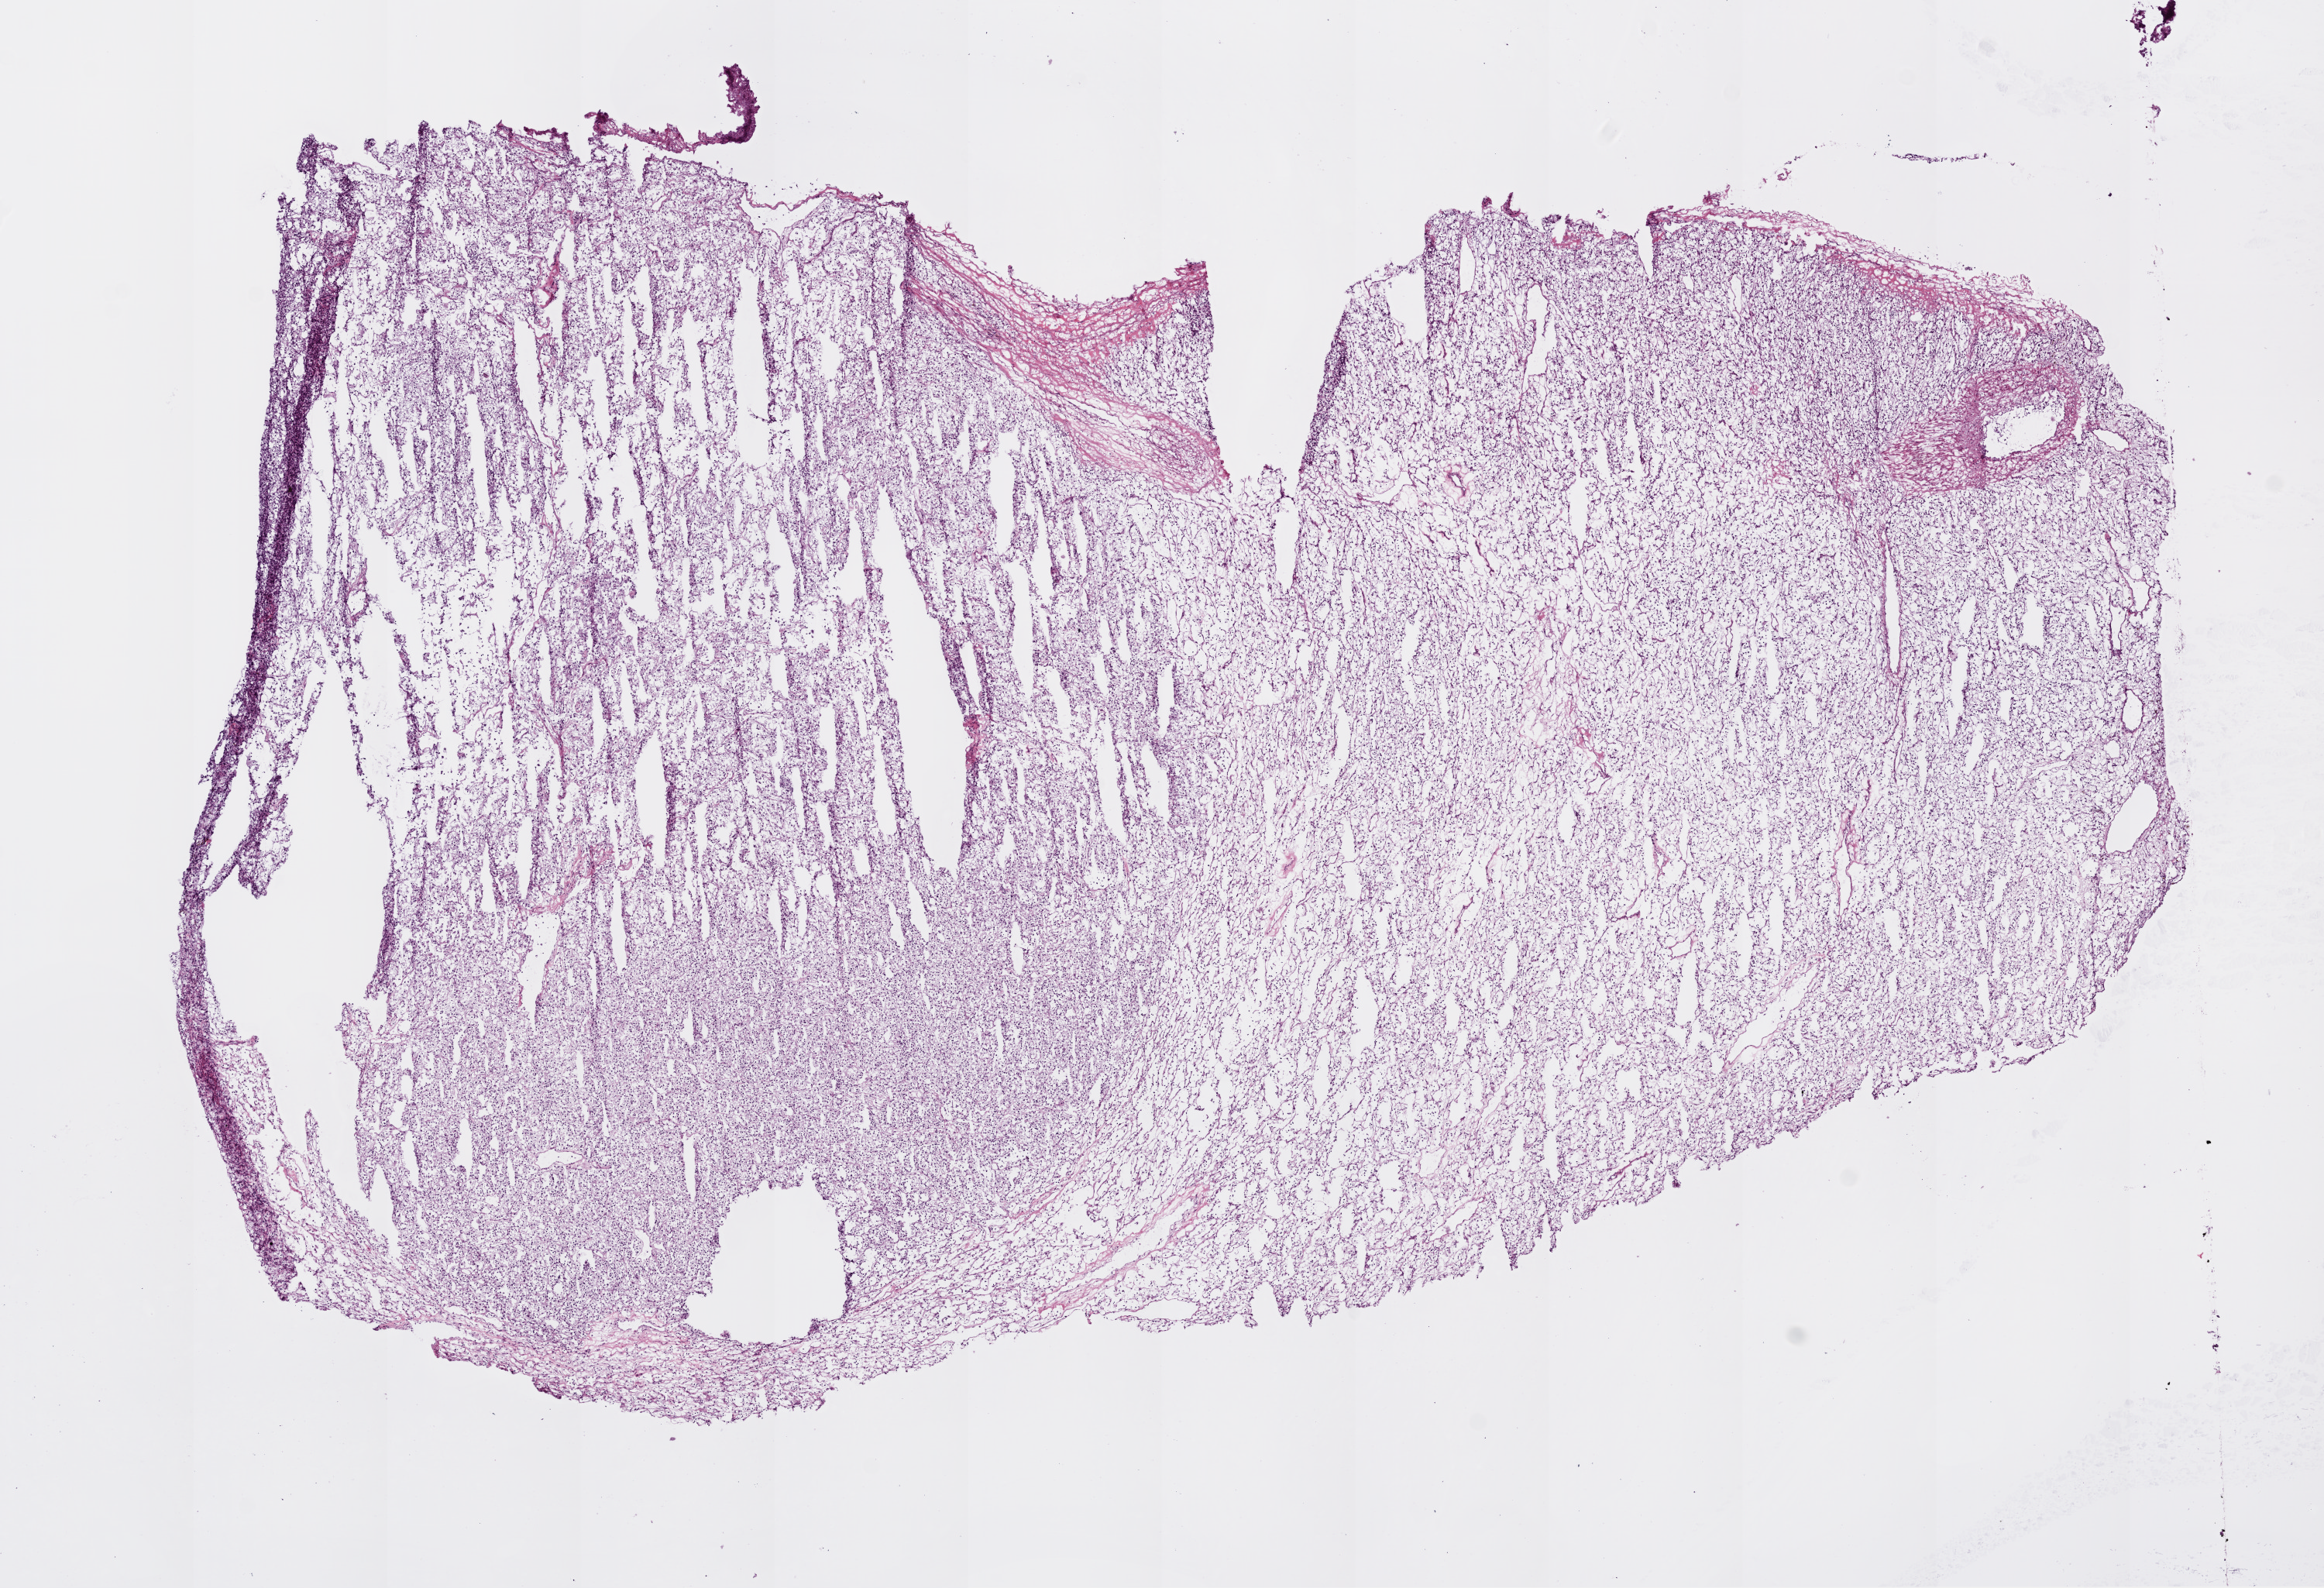
Whole-slide histology image, Hematoxylin and eosin (H&E) stained, shown as a low-resolution overview of the whole scanned area (about 12.0 x 8.2 mm, from a 20x scan), frozen section from the bottom of the tissue portion, sample: primary tumour, kidney. Female patient; age at initial diagnosis 73 years. Histologic grade: G3 (poorly differentiated). Slide review estimates, as recorded: tumour cells 95%, tumour nuclei 85%, normal cells 0%, stromal cells 5%, necrosis 0%.
• diagnosis: Clear cell adenocarcinoma, NOS
• AJCC pathologic stage: IV